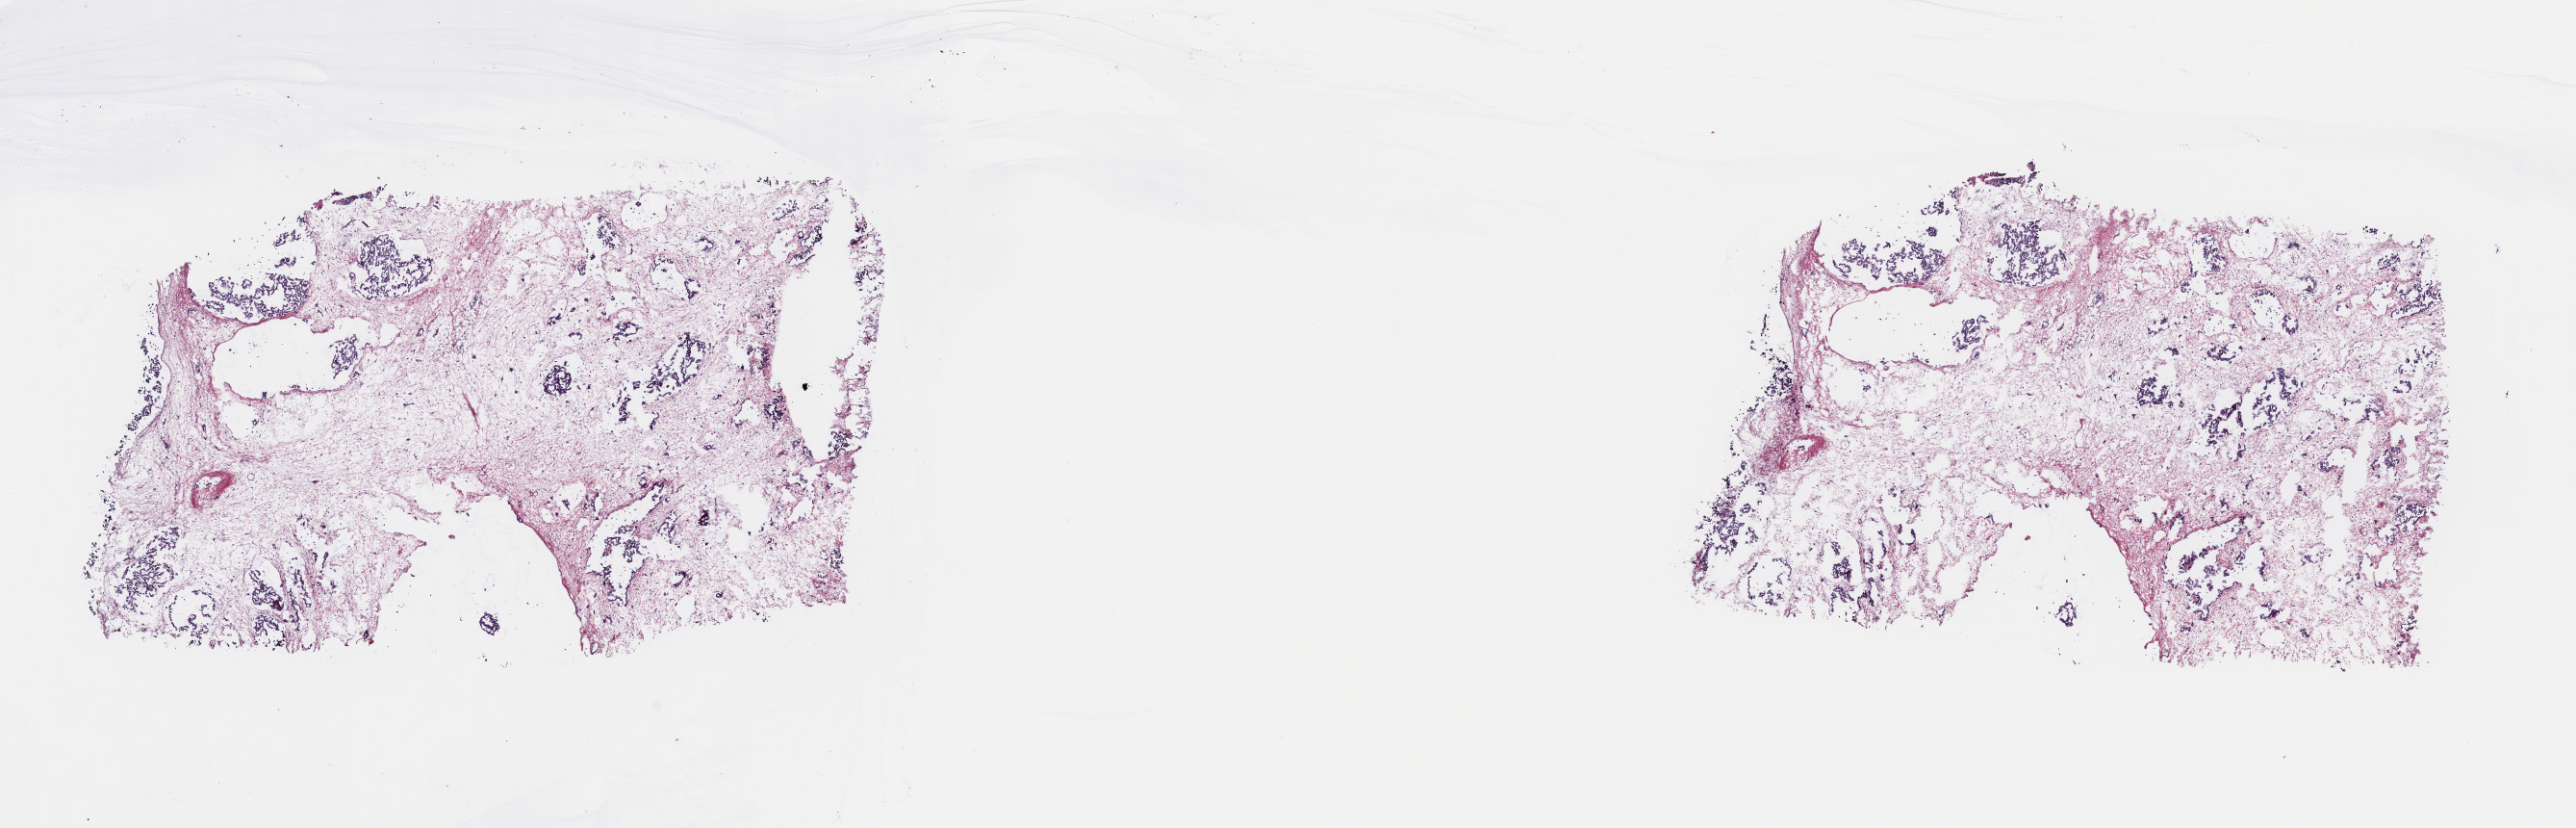
Digitized H&E tissue section (whole slide) — a low-resolution overview of the entire scanned area, about 21.1 x 6.8 mm (slide scanned at 40x). Frozen section from the top of the tissue portion. Primary tumour sample from the mesothelium. Male, age 54 years at initial diagnosis. Slide review estimates, as recorded: tumour cells 15%, tumour nuclei 60%, normal cells 0%, stromal cells 85%, necrosis 0%. Infiltration values recorded for this section: lymphocyte infiltration 0%, monocyte infiltration 0%, neutrophil infiltration 0%.
- AJCC pathologic stage: II
- histologic diagnosis: Epithelioid mesothelioma, malignant (pleura, NOS)